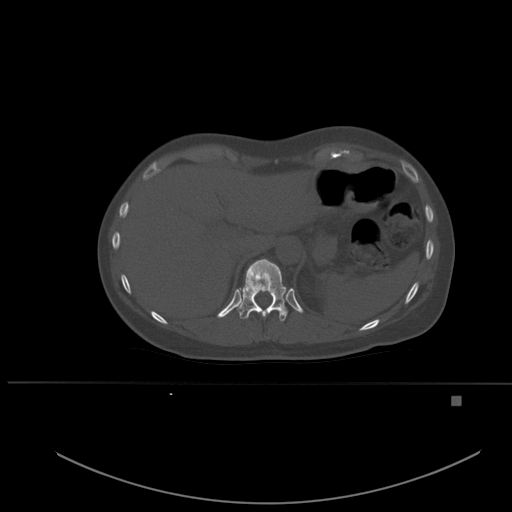
CT including the spine, one axial slice. Bone window (W 1800 / L 400 HU). 512 × 512 image matrix. Female patient, age 49 years. From the clinical record (not read from this slice): primary cancer: breast.
Annotated regions visible in this slice (semi-automatically segmented with operator editing):
- T11 vertebra: bounding box (x1, y1, x2, y2) in pixels: (237, 259, 288, 321)